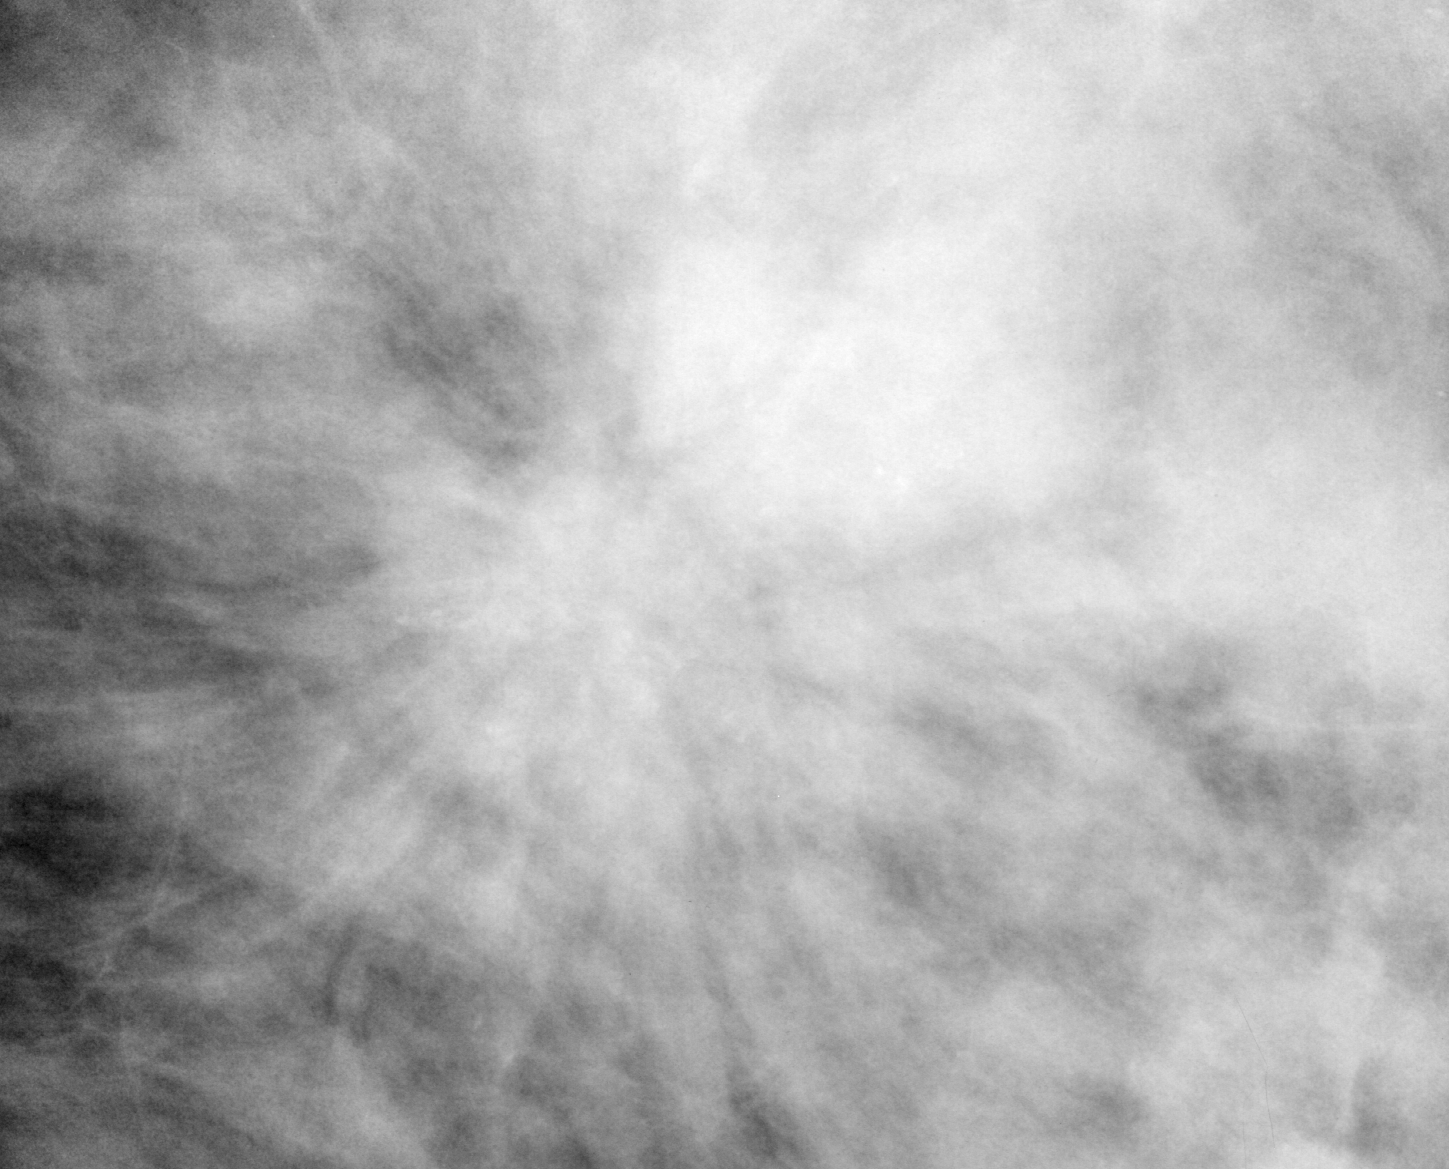
Crop from a digitized film mammogram around one marked abnormality; left breast; MLO view.
- Marked abnormality: calcifications, morphology pleomorphic, distribution clustered; BI-RADS assessment category 5; subtlety rating 3 on a 1 (subtle) to 5 (obvious) scale; pathology result (as recorded, not read from the image): malignant.